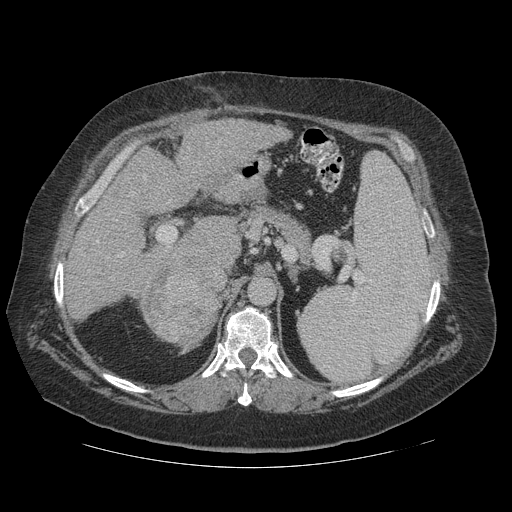
Contrast-enhanced abdominal CT (liver protocol), one axial slice; position 72 of 121 along the scan axis; 140 kVp; soft-tissue window (W 400 / L 40 HU); 2.5 mm slice thickness; 512 × 512 image matrix, field of view 420 × 420 mm. From the clinical record (not read from this slice): diagnosis: hepatocellular carcinoma (patient treated with transarterial chemoembolisation; whether this scan precedes or follows treatment is not stated here); TNM stage (as recorded): Stage-IIIA; Child-Pugh class: A; tumour differentiation: well differentiated; tumour nodularity: multinodular.
Annotated regions visible in this slice (semi-automatically segmented with operator editing):
- liver parenchyma outside the tumour (the mass and vessels are separate outlines, so this box may not span the whole liver): bounding box [x1, y1, x2, y2] px = [66, 120, 291, 308]
- mass: [138, 253, 218, 347]
- liver vessels: [88, 140, 221, 275]